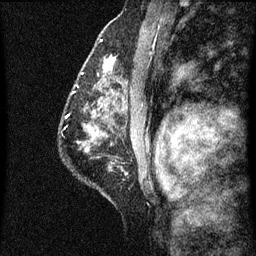
Breast MRI (dynamic contrast-enhanced), one sagittal slice; position 42 of 60 along the scan axis; dynamic contrast-enhanced series, image 2 of 7 at this slice position (ordered by acquisition); 1.5 T; TE 4.2 ms, TR 8 ms; 2 mm slice thickness; 256 × 256 image matrix. Female patient, age 51 years.
Outlined on this slice (semi-automatically segmented with operator editing):
- analysis volume of interest (the breast-tissue region the enhancement analysis was run in; not a lesion): bounding box [x1, y1, x2, y2] px = [86, 52, 125, 101]
- tumour enhancement mask (voxels above the 70 % enhancement threshold inside the analysis volume of interest): [104, 58, 116, 69]